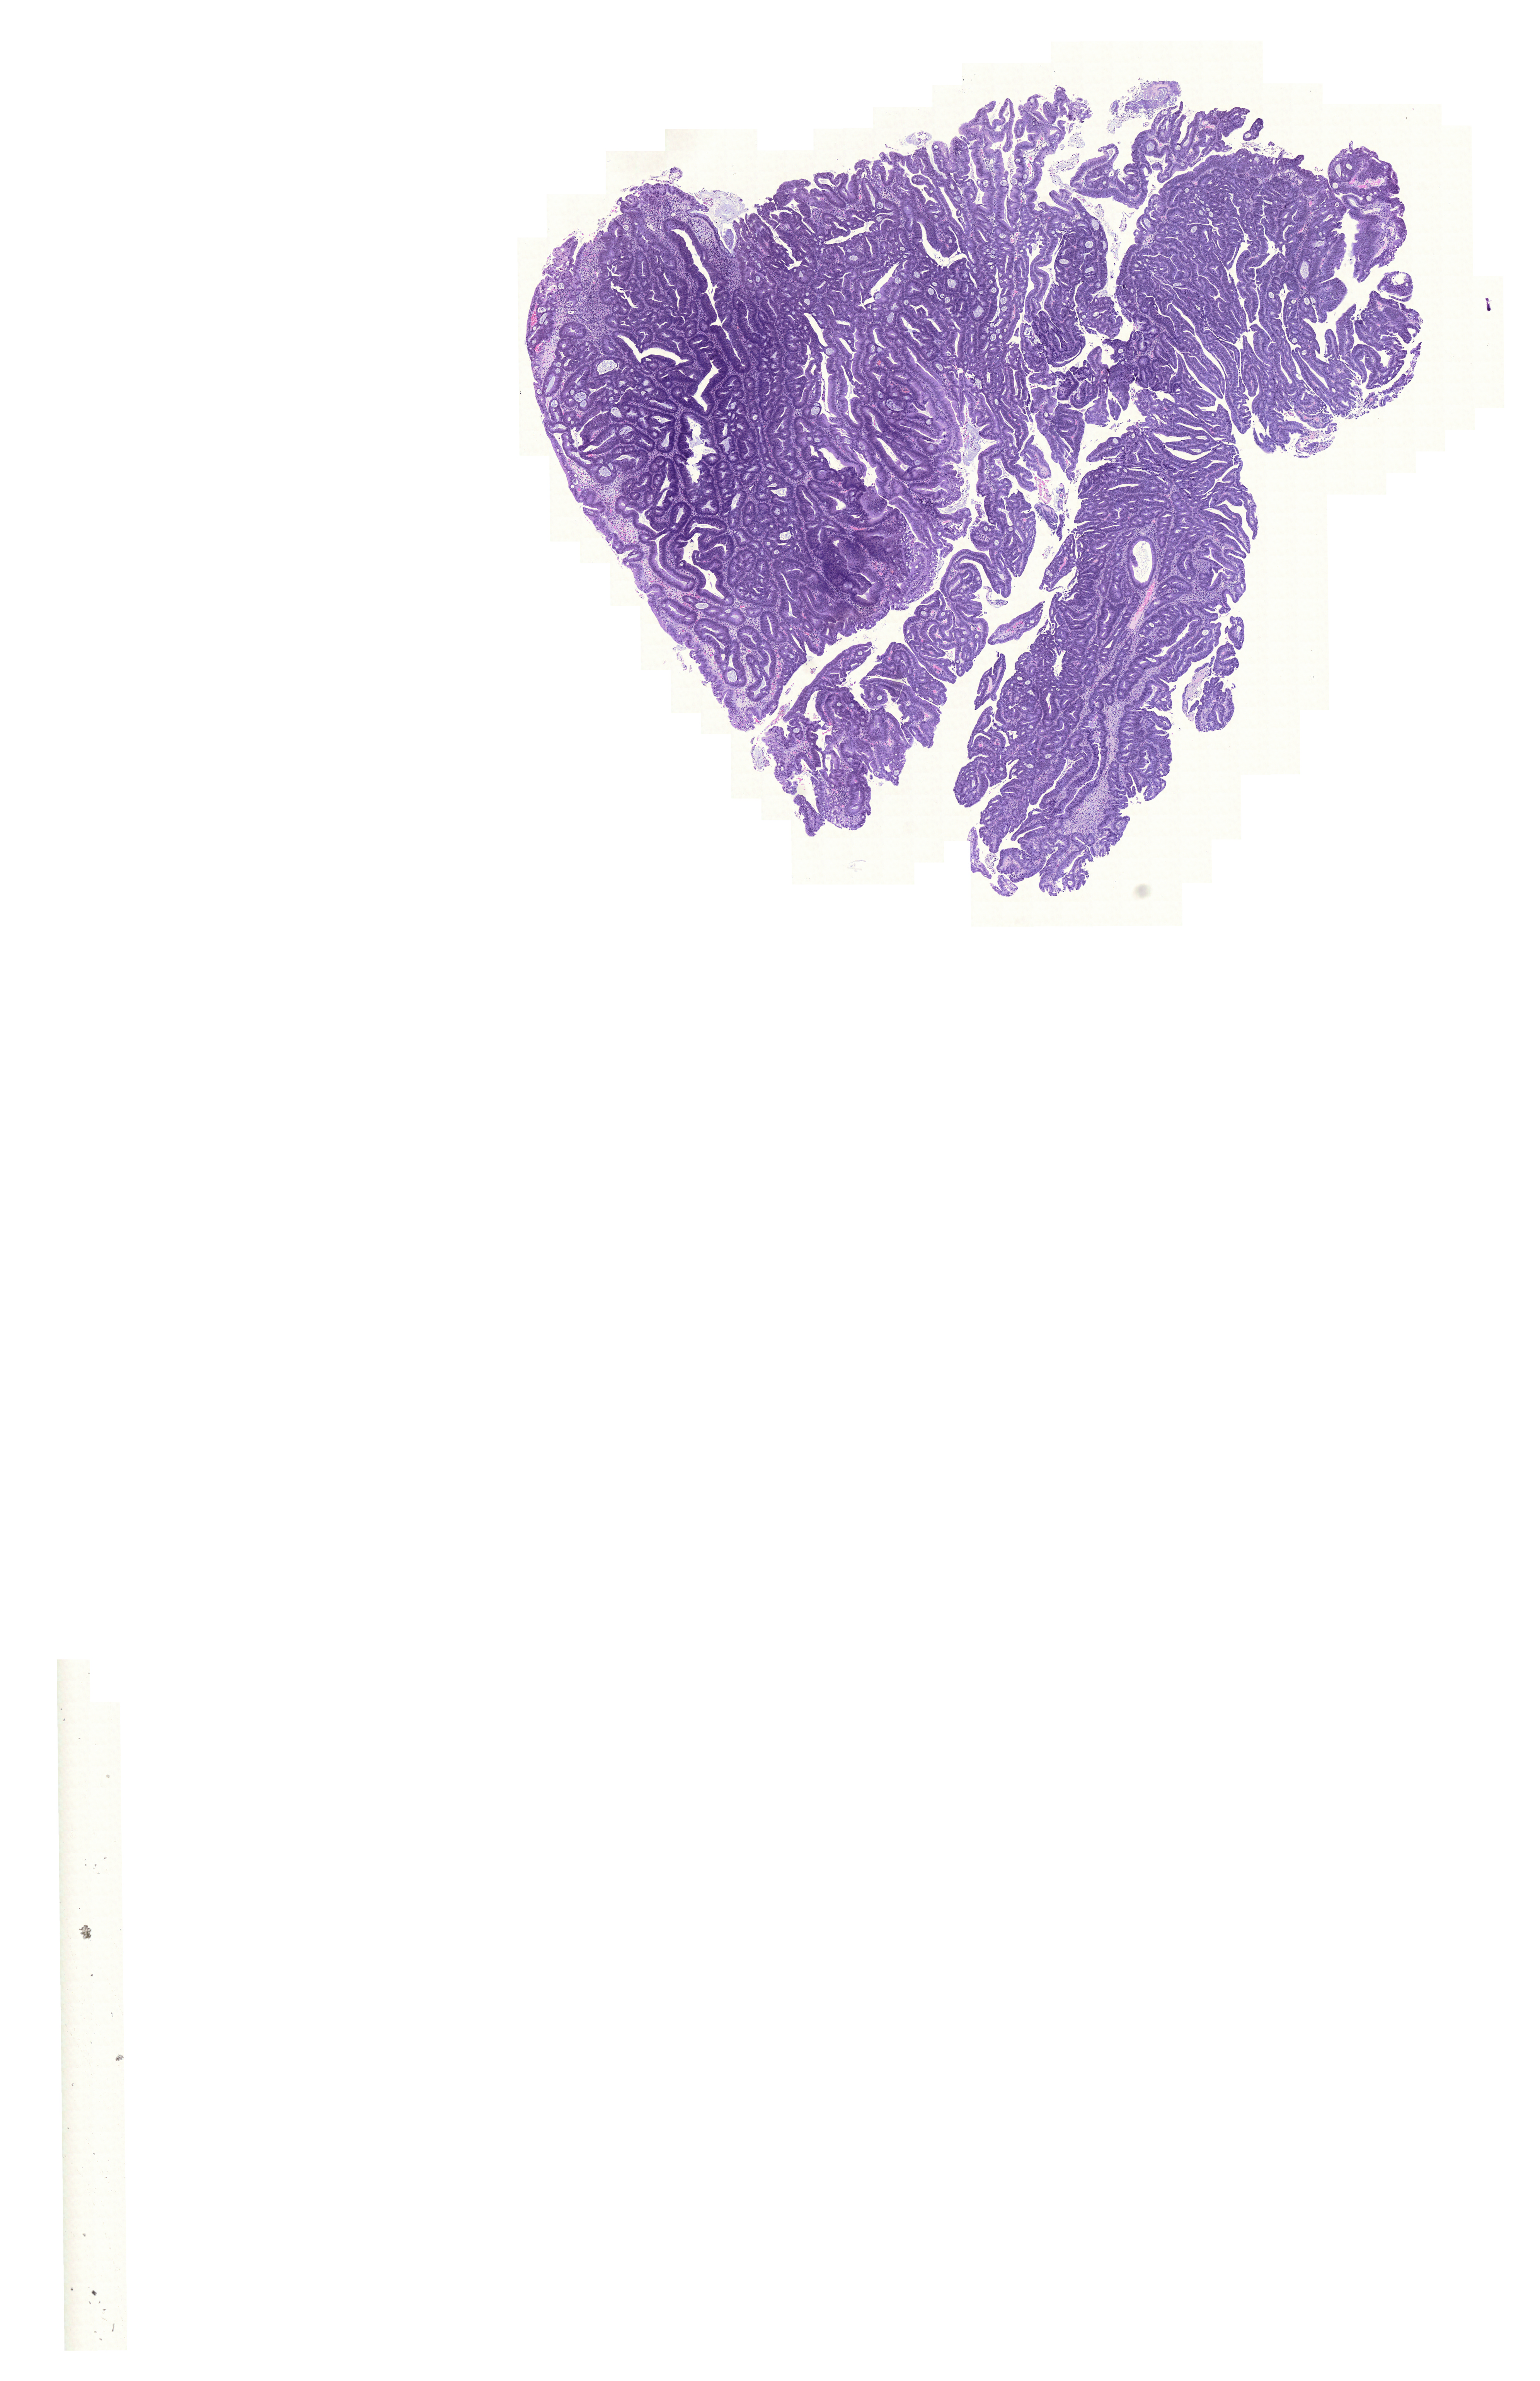
Whole-slide histology image, H&E — a low-resolution overview of the entire scanned area, about 14.8 x 22.9 mm (acquisition: 20x scan); FFPE section; colon, primary tumour sample. Patient: female, age at initial diagnosis 66 years.
Lymph nodes positive (case pathology): 1 of 31 examined. AJCC pathologic stage: IIIB (6th edition). Diagnosis: Adenocarcinoma, NOS (sigmoid colon).